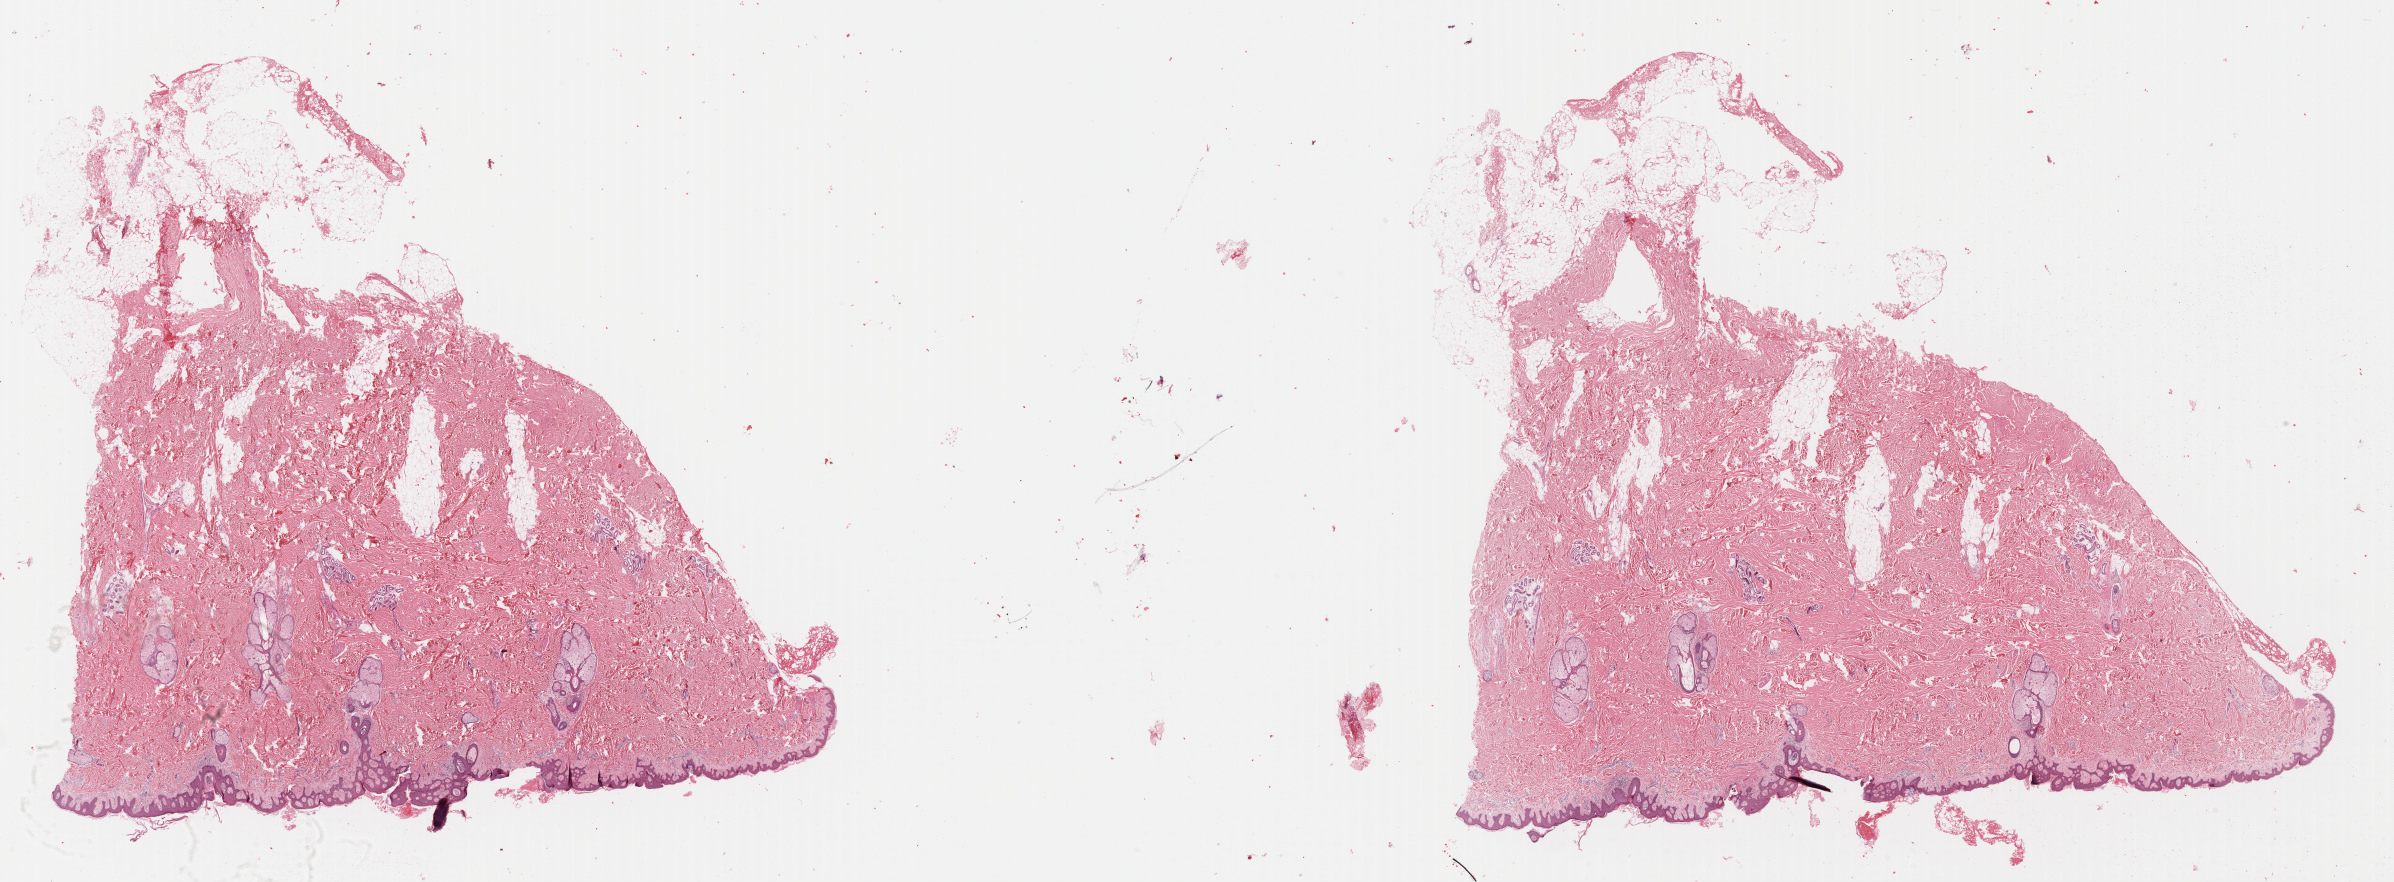
Digitized H&E-stained tissue section (whole slide), low-resolution overview of the scanned area, about 37.6 x 13.9 mm (from a 40x scan). Formalin-fixed paraffin-embedded (FFPE) diagnostic section. Primary tumour sample from the skin. Male patient; age at initial diagnosis 43 years.
* AJCC pathologic stage: IIIA
* diagnosis: Malignant melanoma, NOS